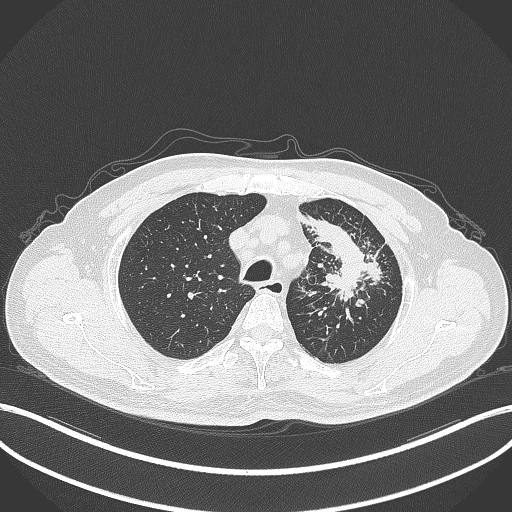
Chest CT, one axial slice. Slice 282 of 386 in the series (ordered by position). Reconstruction kernel B70f. 120 kVp. Lung window (W 1500 / L -600 HU). 512 × 512 image matrix, field of view 400 × 400 mm. Patient: male, 69 years. Case-level facts recorded for this patient, not image findings: clinical TNM (as recorded): T2a N2 M0; histopathological grade: G2-3.
Annotated regions visible in this slice (rectangle marked by the reading radiologist):
- lung tumour (recorded histology: adenocarcinoma): bounding box [x1, y1, x2, y2] px = [301, 207, 386, 300]